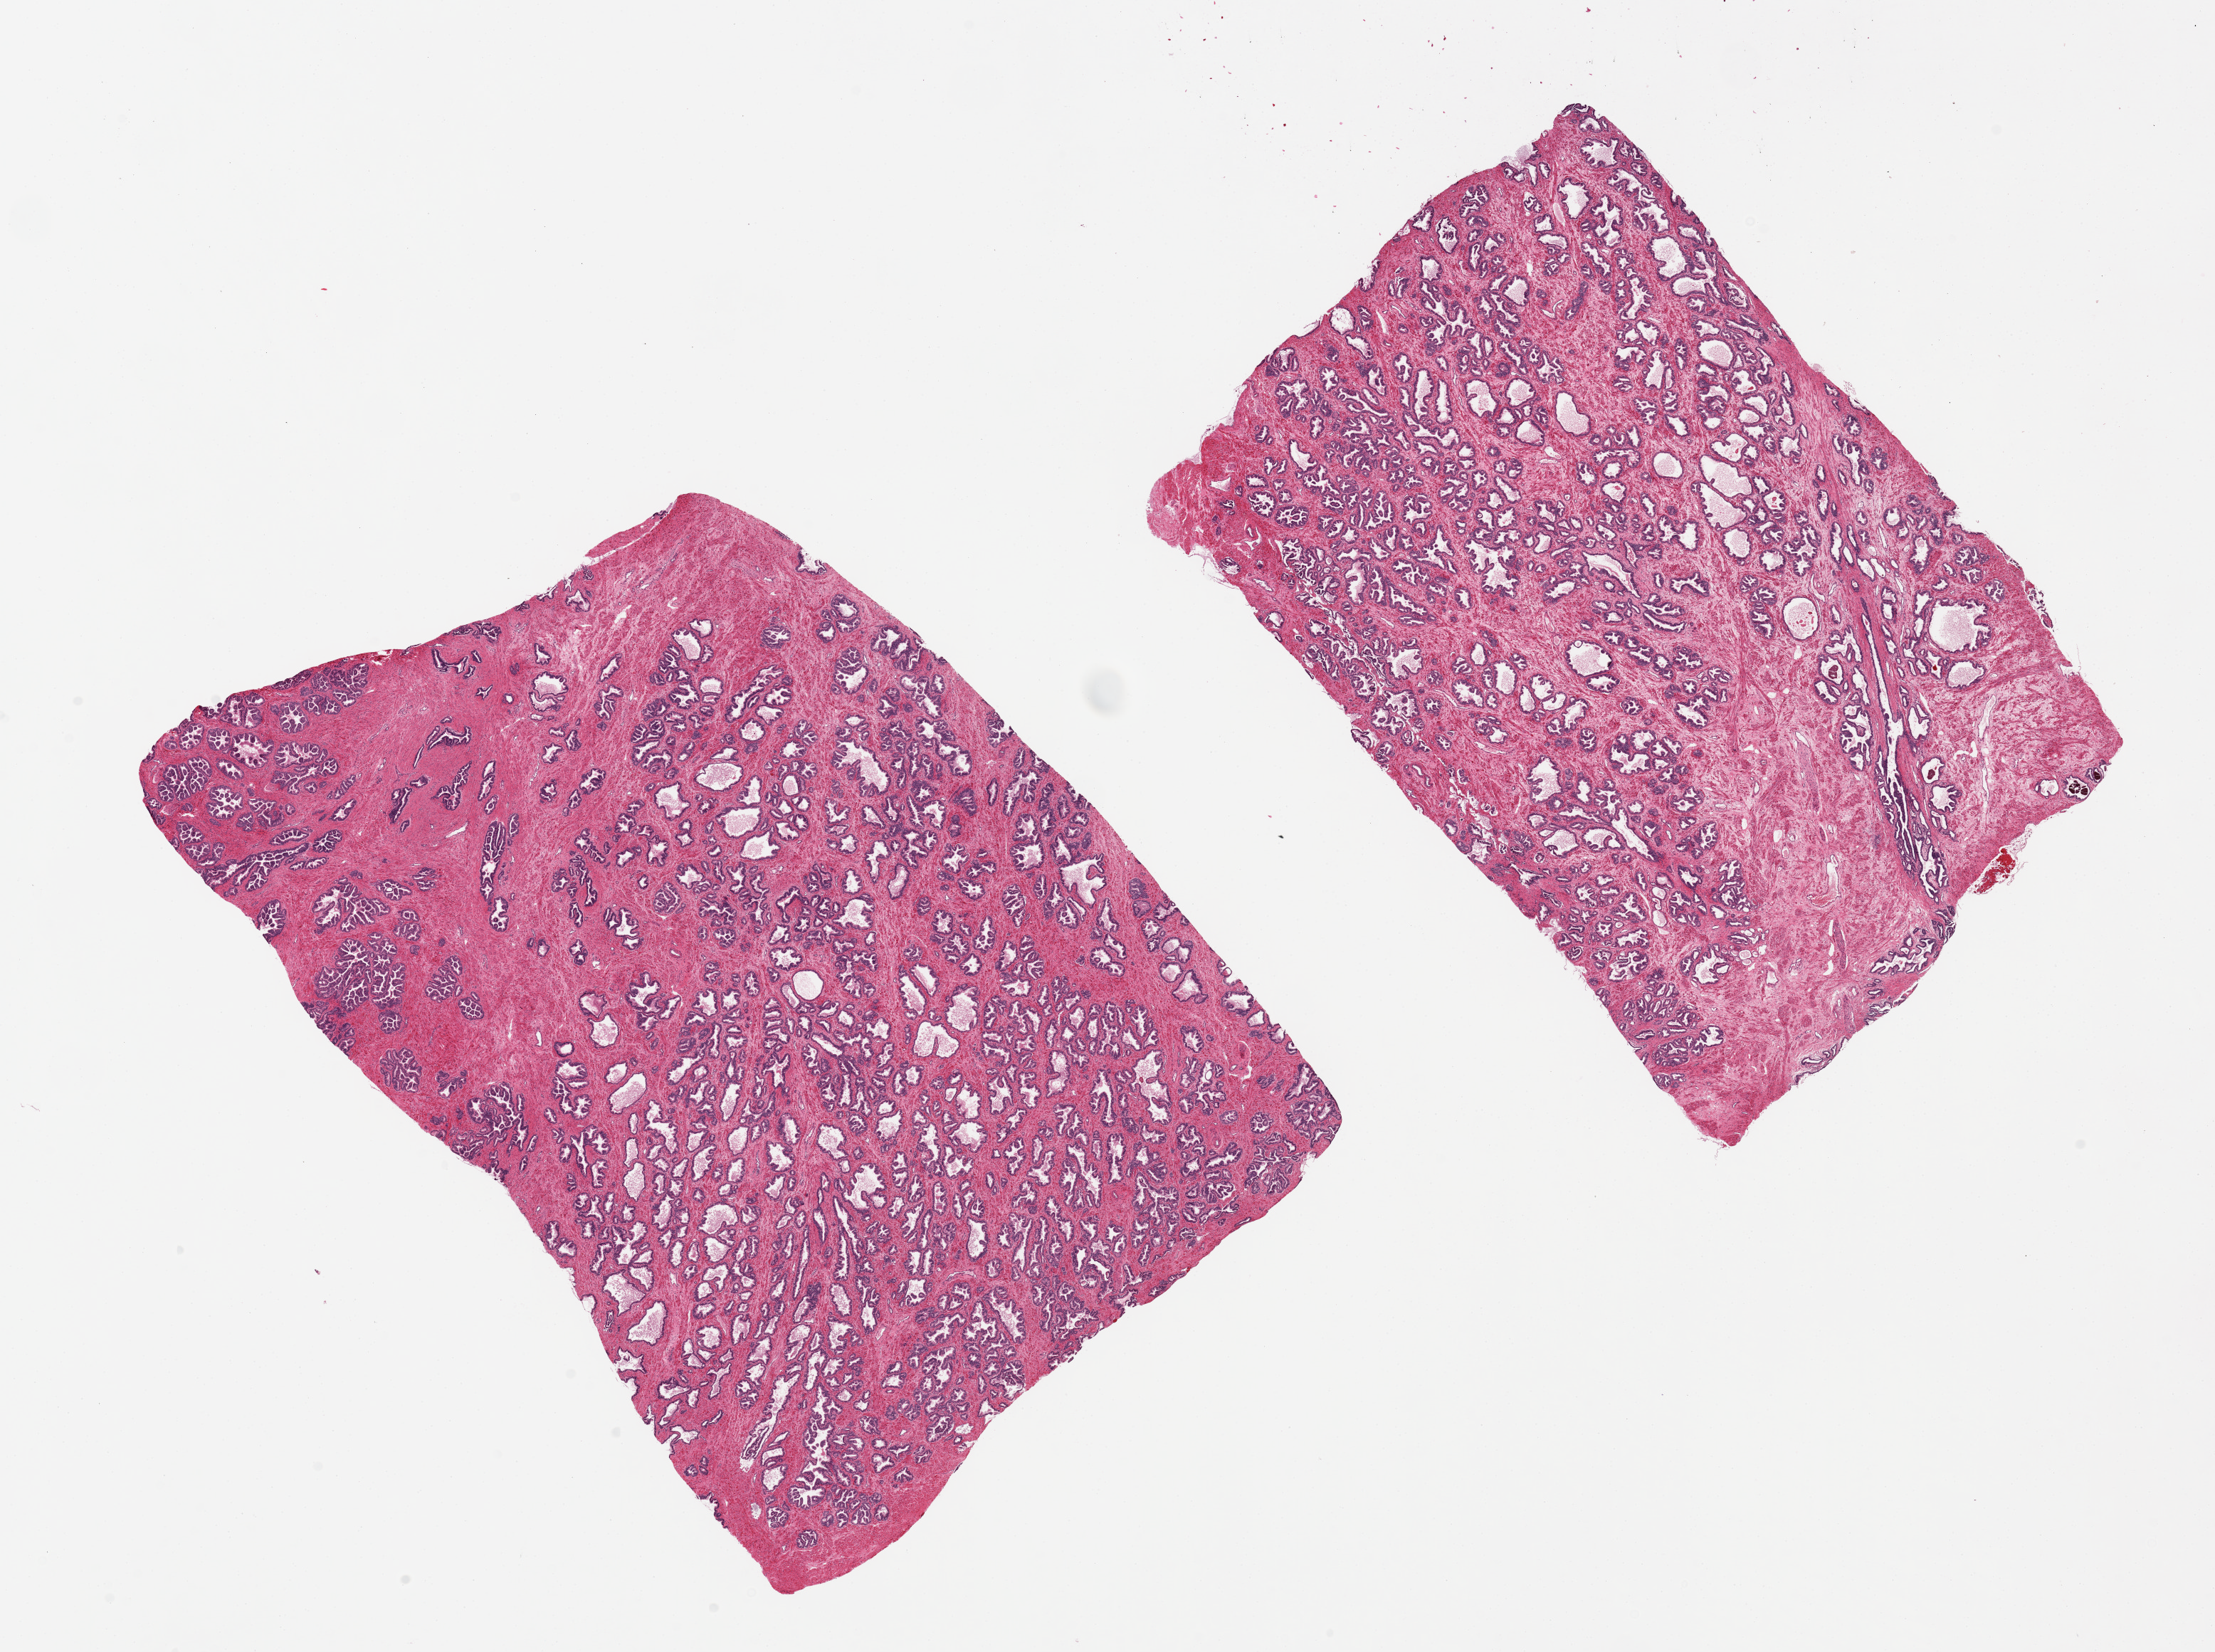
Haematoxylin and eosin whole-slide image, low-resolution overview of the scanned area, about 24.6 x 18.4 mm (from a 20x scan). PAXgene-fixed paraffin-embedded (PFPE) section. Sampled site (target tissue): prostate. Tissue donor sample. Male donor.
Pathologist's review note for this sample: 2 pieces. 12x8.5 & 10x7mm. Good glandular content.